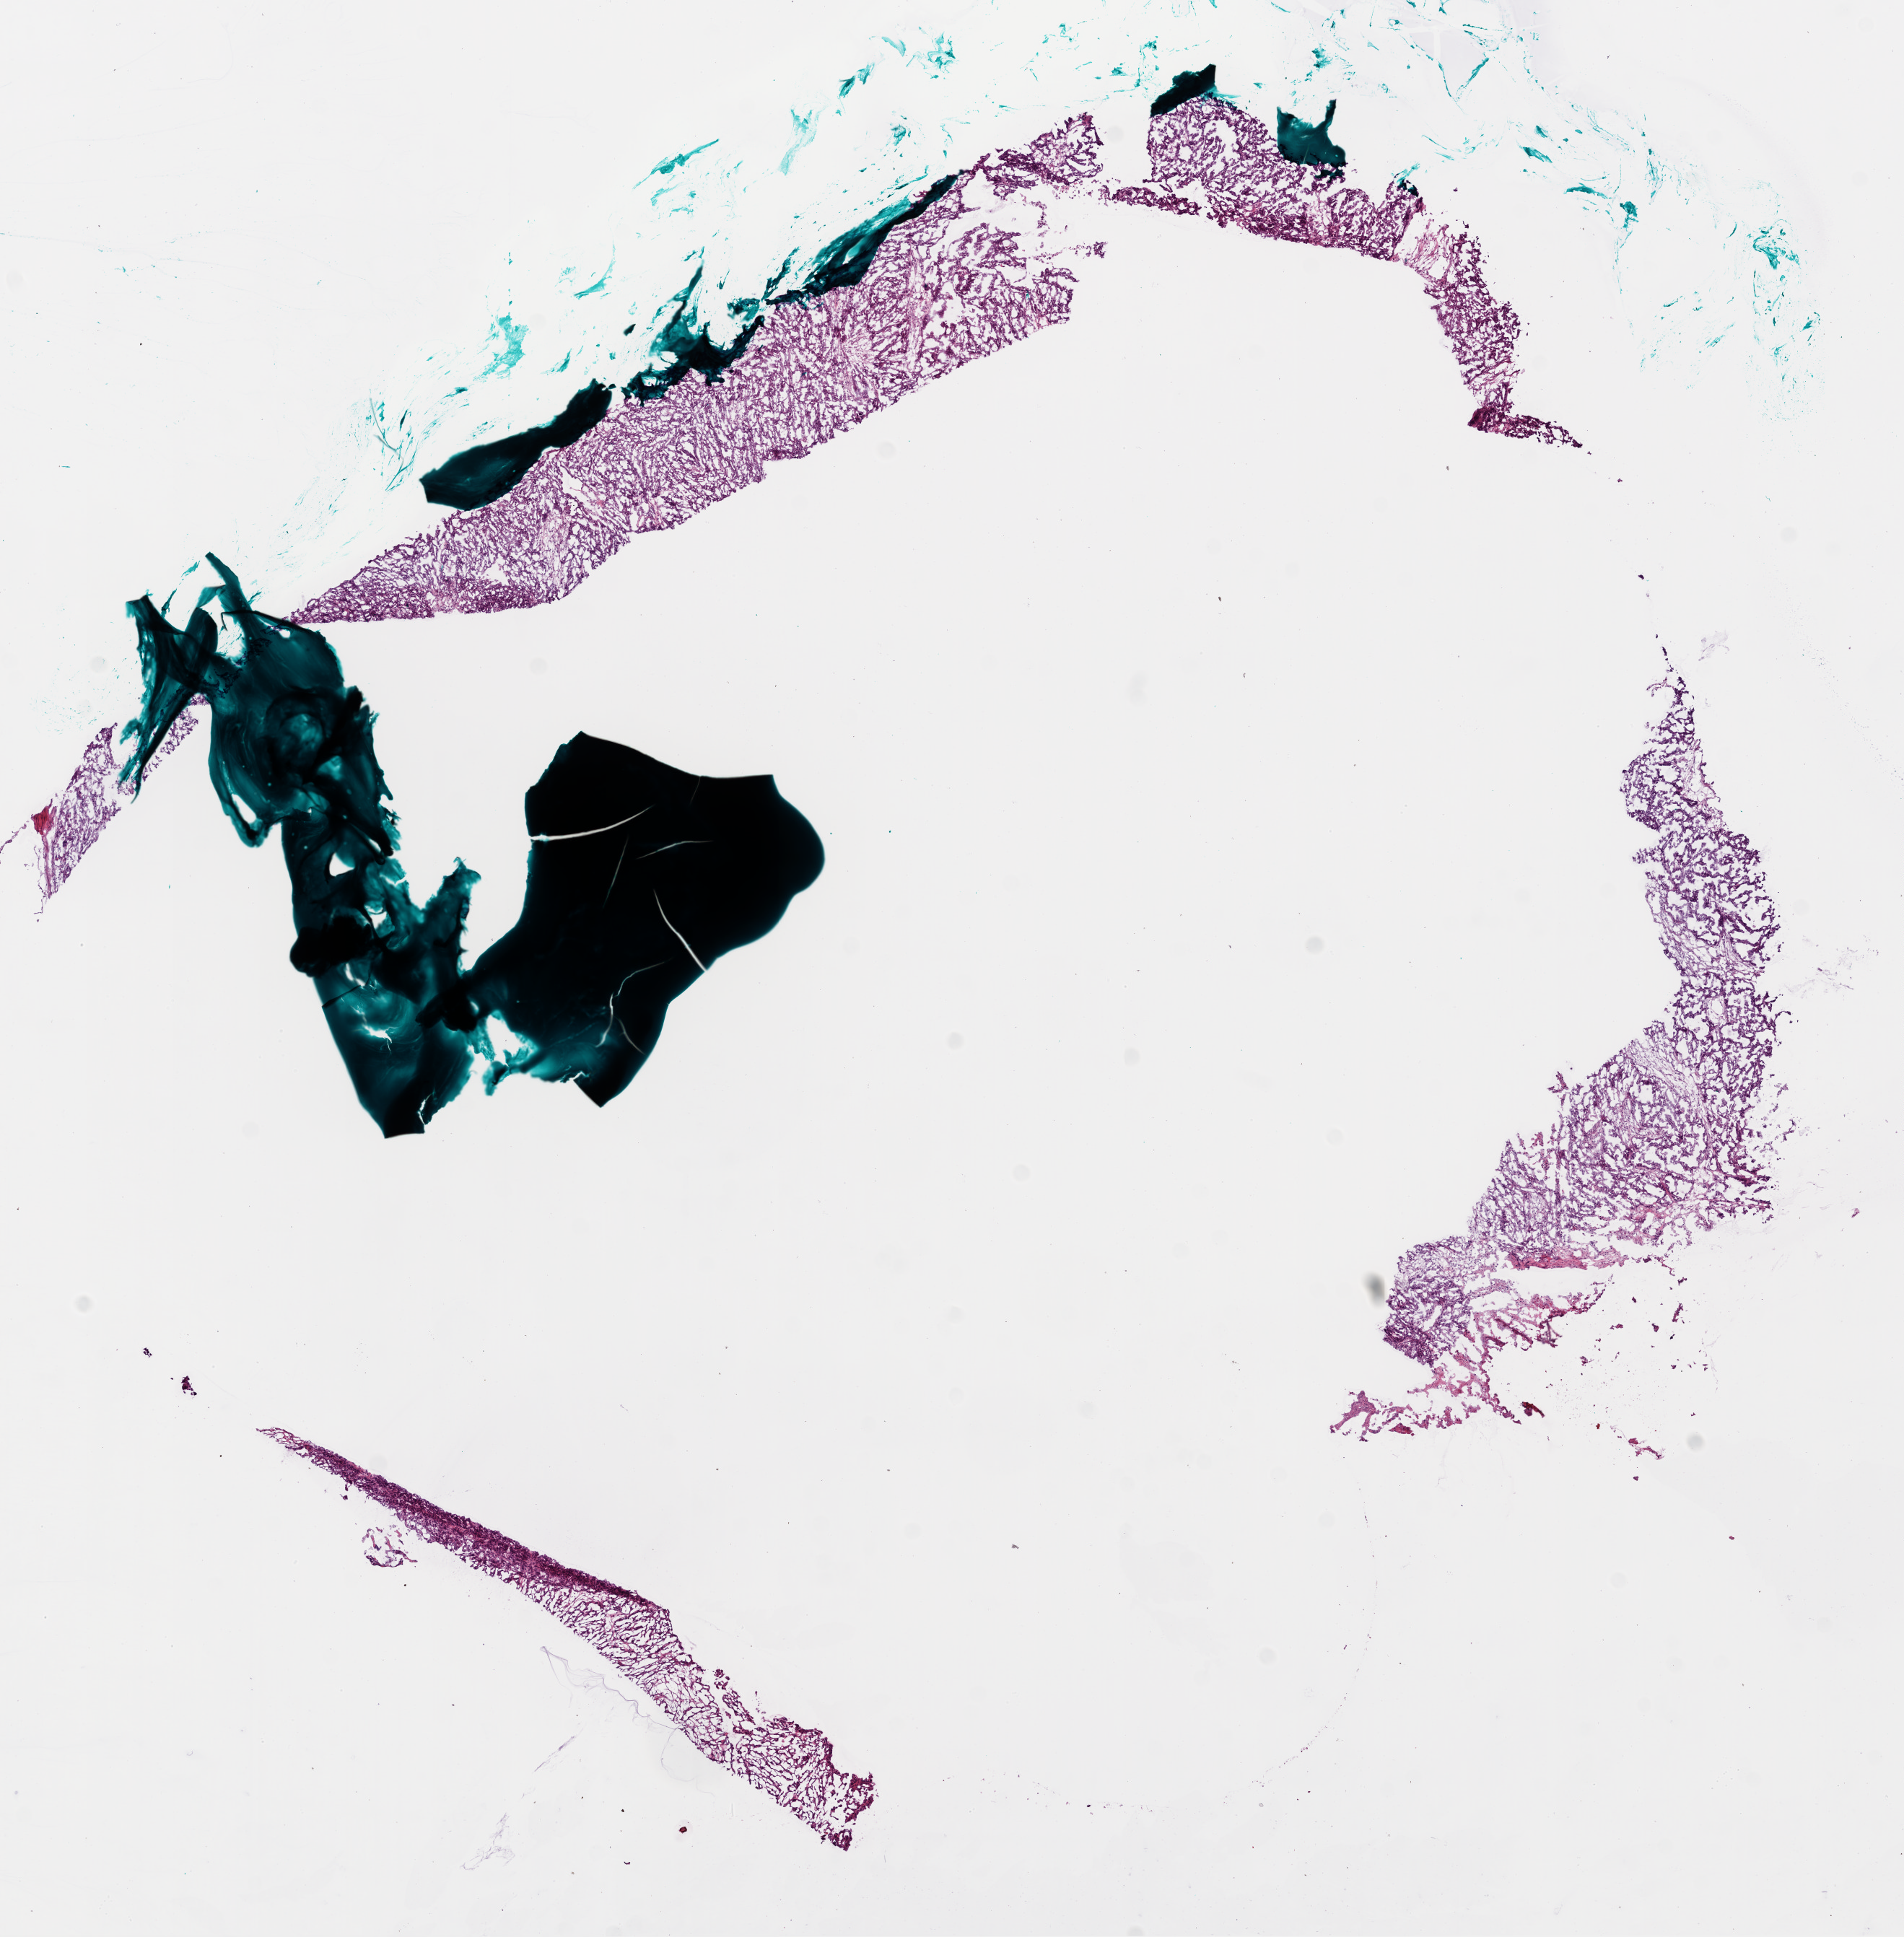
Whole-slide histology image, H&E-stained — shown as a low-resolution overview of the whole scanned area (about 10.6 x 10.8 mm, acquisition: 20x scan). Frozen section from the bottom of the tissue portion. Sample: primary tumour, ovary. Female patient; age at initial diagnosis 65 years. Slide review estimates, as recorded: tumour cells 94%, tumour nuclei 95%.
Pathologic diagnosis: Serous cystadenocarcinoma, NOS.